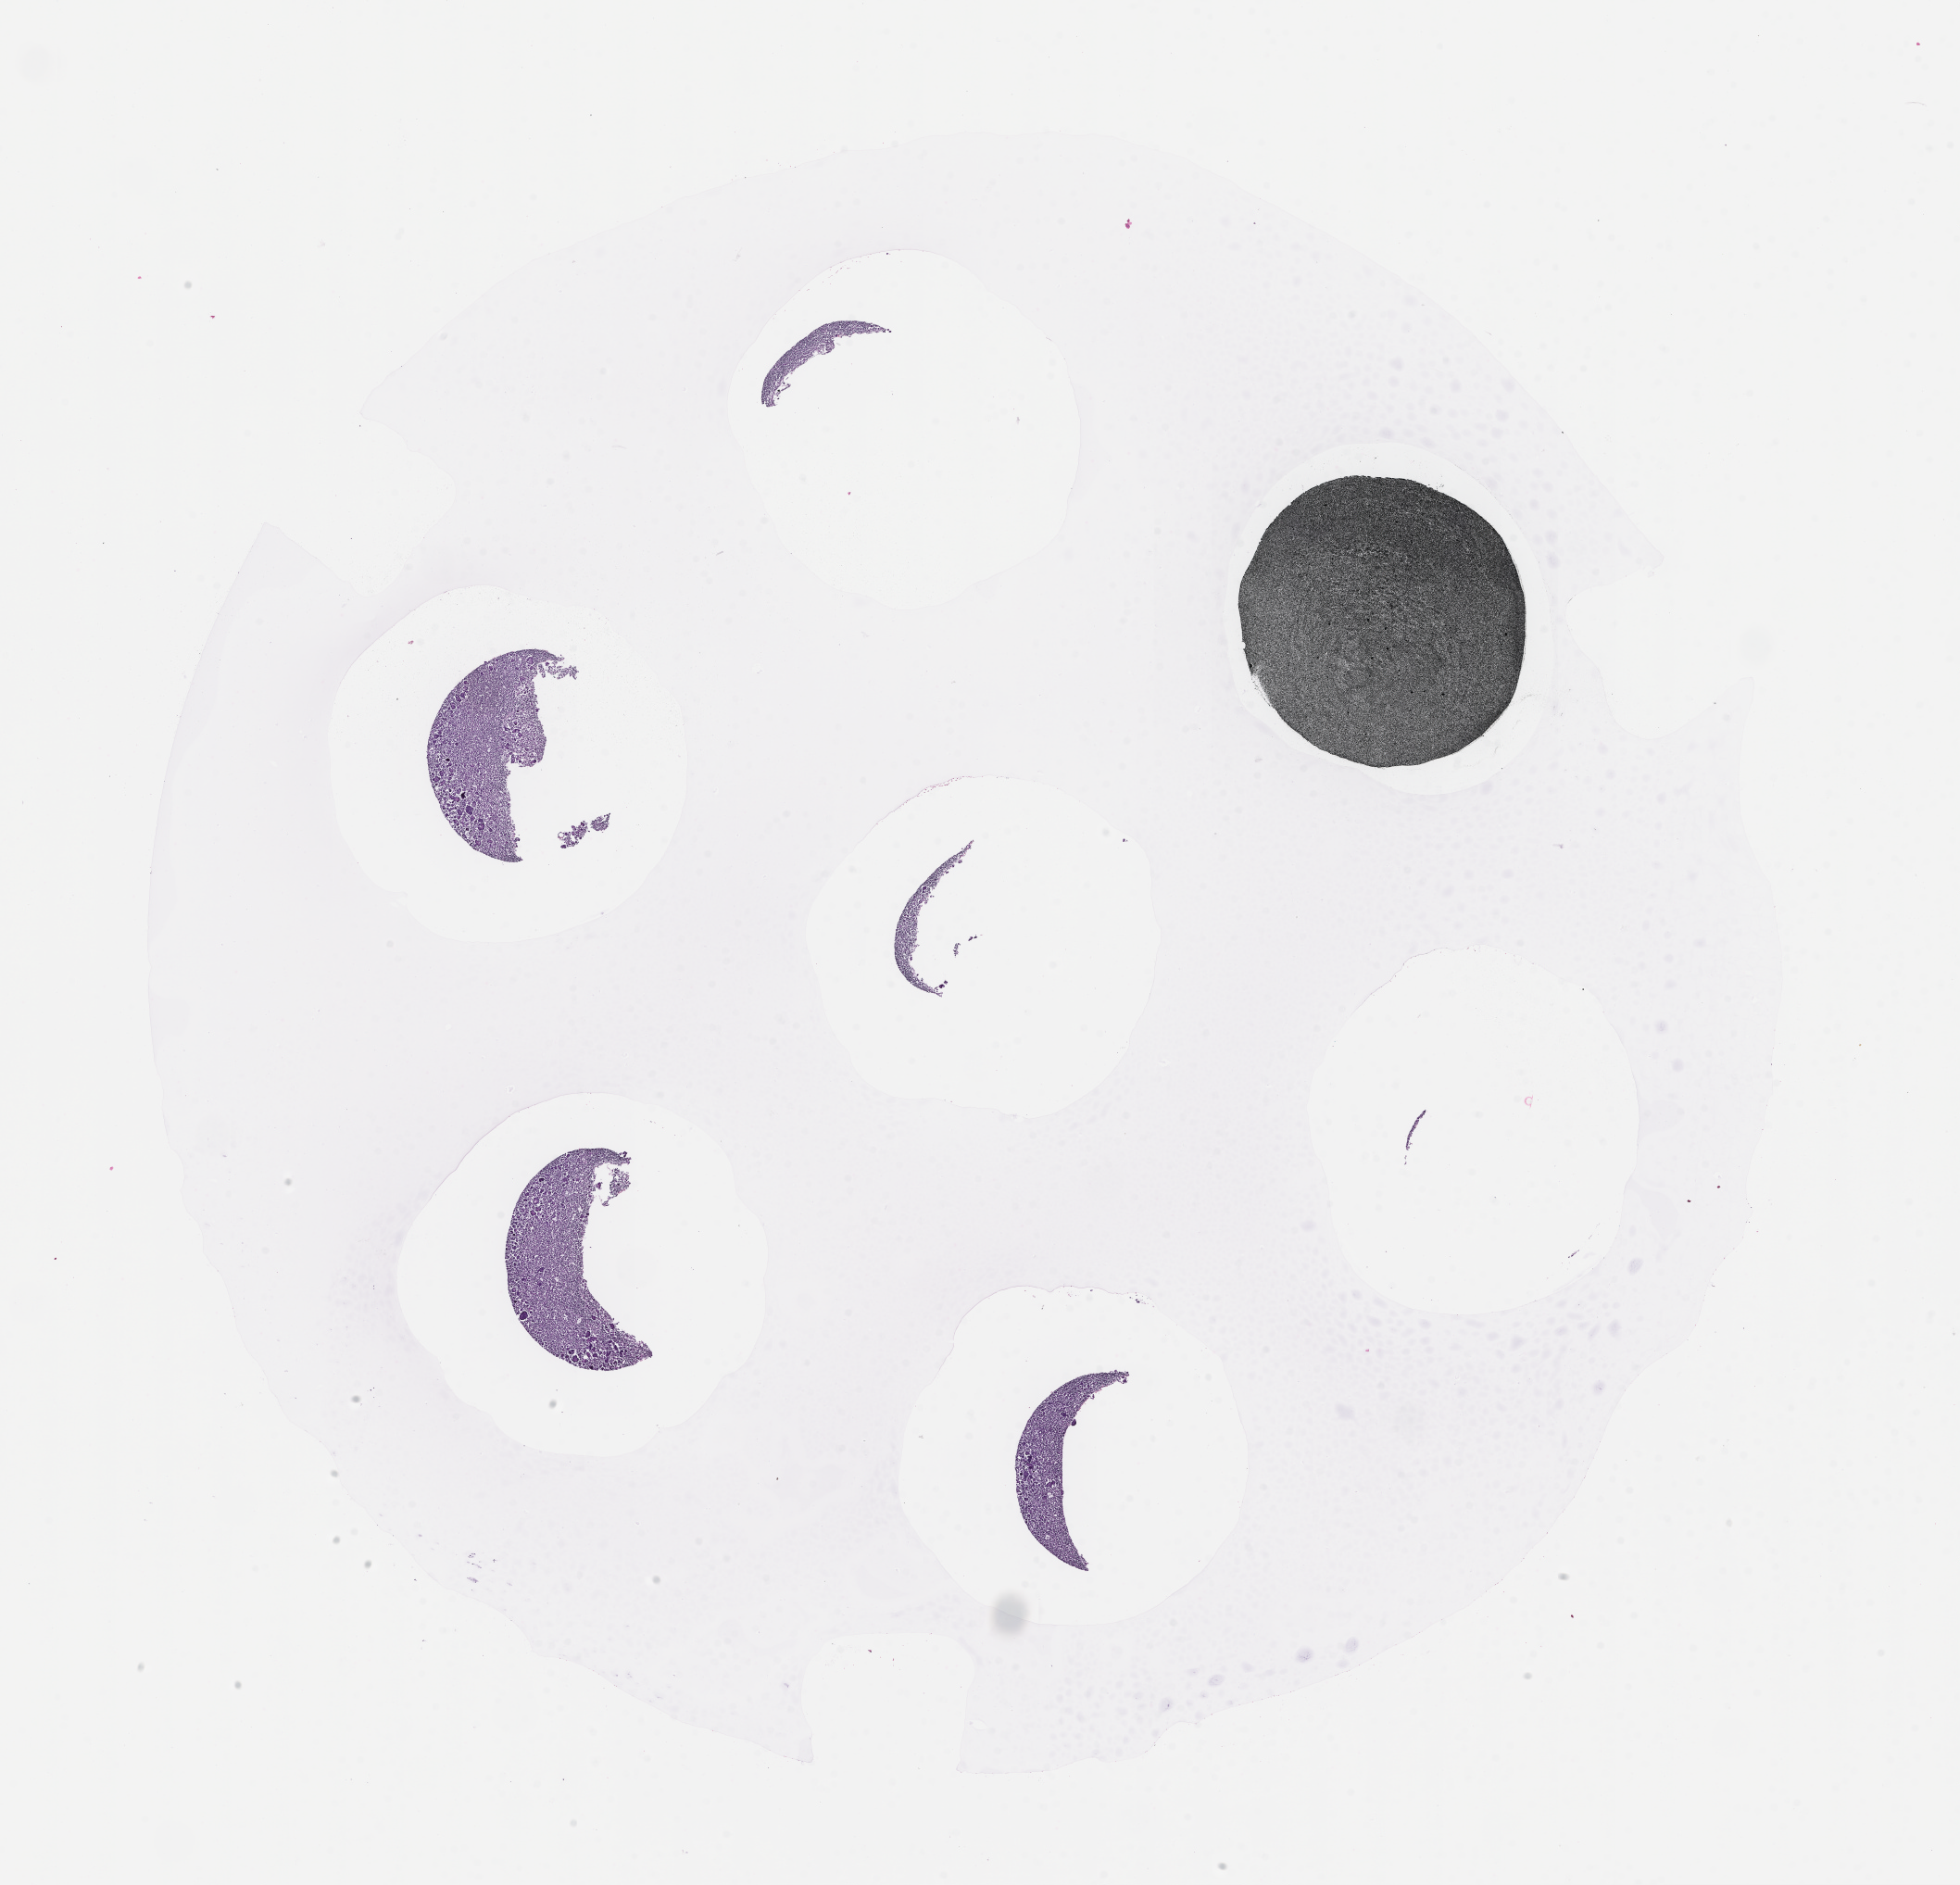
Digitized haematoxylin and eosin-stained section — low-resolution overview of the scanned area, about 17.1 x 16.4 mm; formalin-fixed, paraffin-embedded (FFPE) tissue. Patient sex: female.
• this section: metastatic tumor tissue
• patient diagnosis (primary): Fallopian Tube Carcinoma